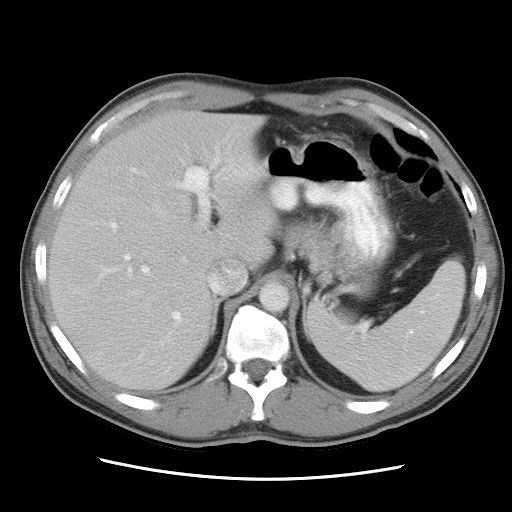
Contrast-enhanced abdominal CT, one axial slice. Slice 21 of 34 in the series (ordered by position). Intravenous contrast given. Soft-tissue window (W 400 / L 40 HU). 512 × 512 image matrix, field of view 360 × 360 mm. Male patient, age 40 years. Case-level facts recorded for this patient, not image findings: diagnosis: colorectal cancer liver metastases, imaged before liver resection; multiple liver metastases: yes; largest metastasis: 1.5 cm; disease in both lobes: yes.
Structures marked on this image (expert manual segmentation):
- liver: bounding box [x1, y1, x2, y2] px = [49, 112, 278, 388]
- planned liver remnant (the part of the liver to remain after resection): [49, 112, 279, 388]
- portal vein (with intrahepatic branches): [104, 167, 213, 322]